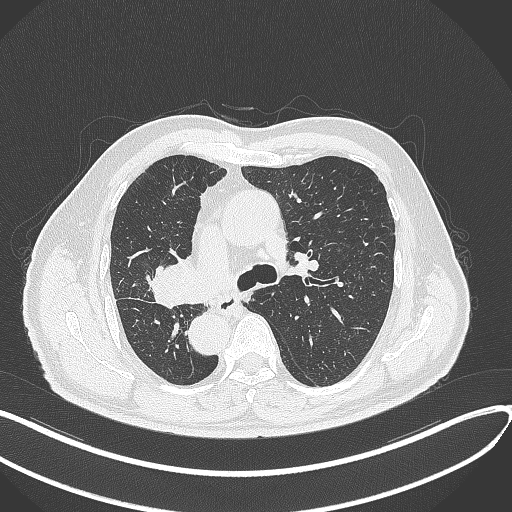
Chest CT, one axial slice; position 194 of 300 along the scan axis; reconstruction kernel B70f; 120 kVp; lung window (W 1500 / L -600 HU); 1 mm slice thickness; 512 × 512 image matrix. Male patient, age 67 years. From the clinical record (not read from this slice): clinical TNM (as recorded): T2a N0 M0.
Annotated regions visible in this slice (rectangle marked by the reading radiologist):
- lung tumour (recorded histology: squamous cell carcinoma): bounding box <146,256,199,311> (left, top, right, bottom; pixels)